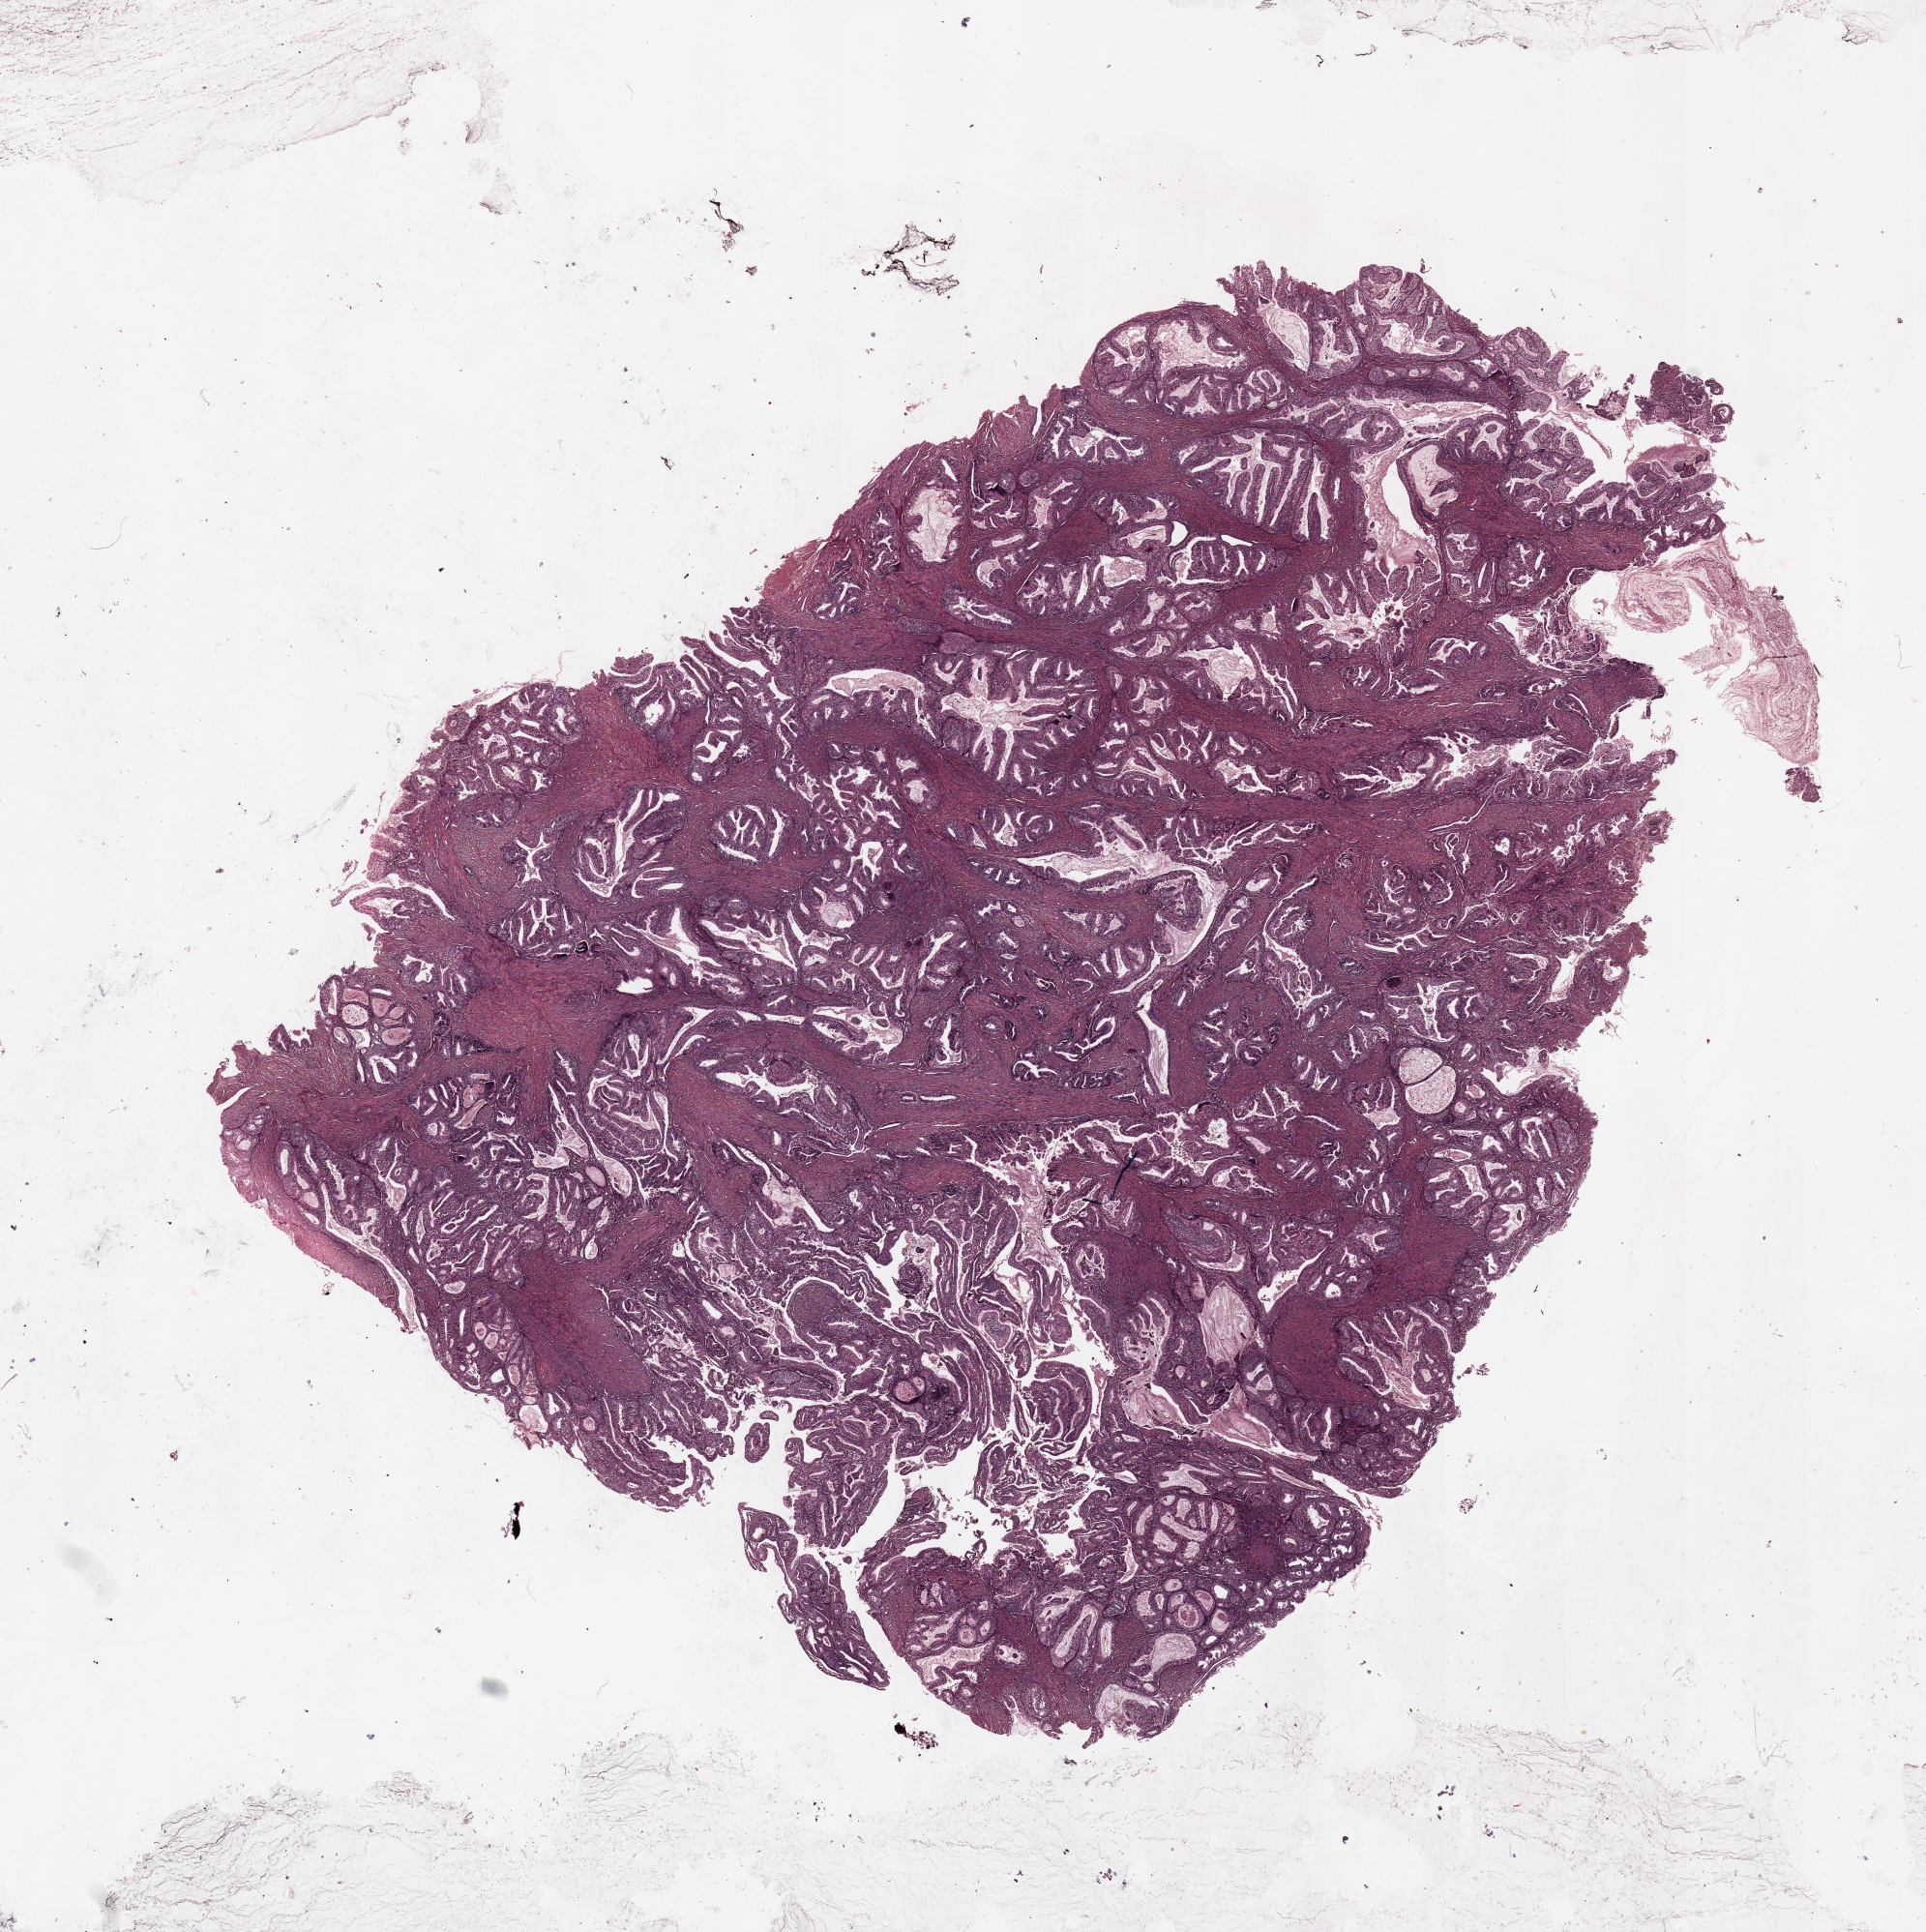
Digitized Hematoxylin and eosin (H&E) stained tissue section (whole slide), a low-resolution overview of the entire scanned area, about 15.8 x 15.8 mm (acquisition: 20x scan). Uterus, tumour tissue. Patient: female, age 58 years. Histologic grade: G1 (well differentiated).
AJCC pathologic stage: I. Diagnosis: Endometrioid adenocarcinoma, NOS.